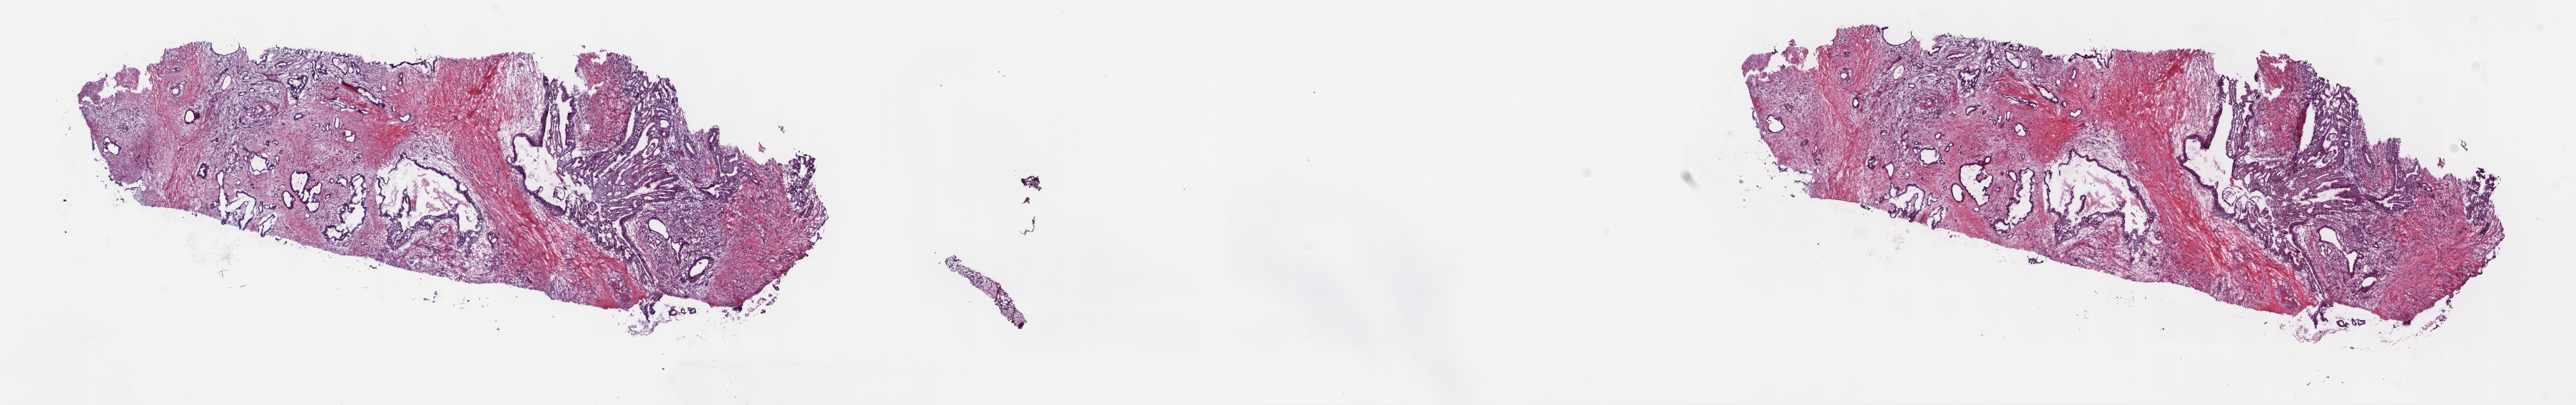
H&E whole-slide image, low-resolution overview of the scanned area, about 29.2 x 4.6 mm (slide scanned at 40x), frozen section from the top of the tissue portion, primary tumour sample from the pancreas. Male patient; age at initial diagnosis 85 years. Composition of this section per pathologist review: tumour cells 45%, tumour nuclei 88%.
Pathologic diagnosis: Infiltrating duct carcinoma, NOS (tail of pancreas).